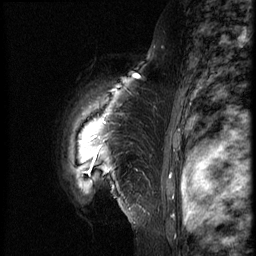
Breast MRI (dynamic contrast-enhanced), one sagittal slice; dynamic contrast-enhanced series, image 2 of 3 at this slice position (ordered by acquisition); 1.5 T; TE 4.2 ms, TR 8.9 ms; 2.5 mm slice thickness; 256 × 256 image matrix, field of view 200 × 200 mm. Female patient, age 39 years. From the clinical record (not read from this slice): setting: breast cancer imaged before/during neoadjuvant chemotherapy; receptor status: HER2-positive.
Annotated regions visible in this slice (semi-automatically segmented with operator editing):
- analysis volume of interest (the breast-tissue region the enhancement analysis was run in; not a lesion): bounding box (x1, y1, x2, y2) in pixels: (56, 75, 163, 218)
- tumour enhancement mask (voxels above the 140 % enhancement threshold inside the analysis volume of interest): (85, 75, 141, 173)